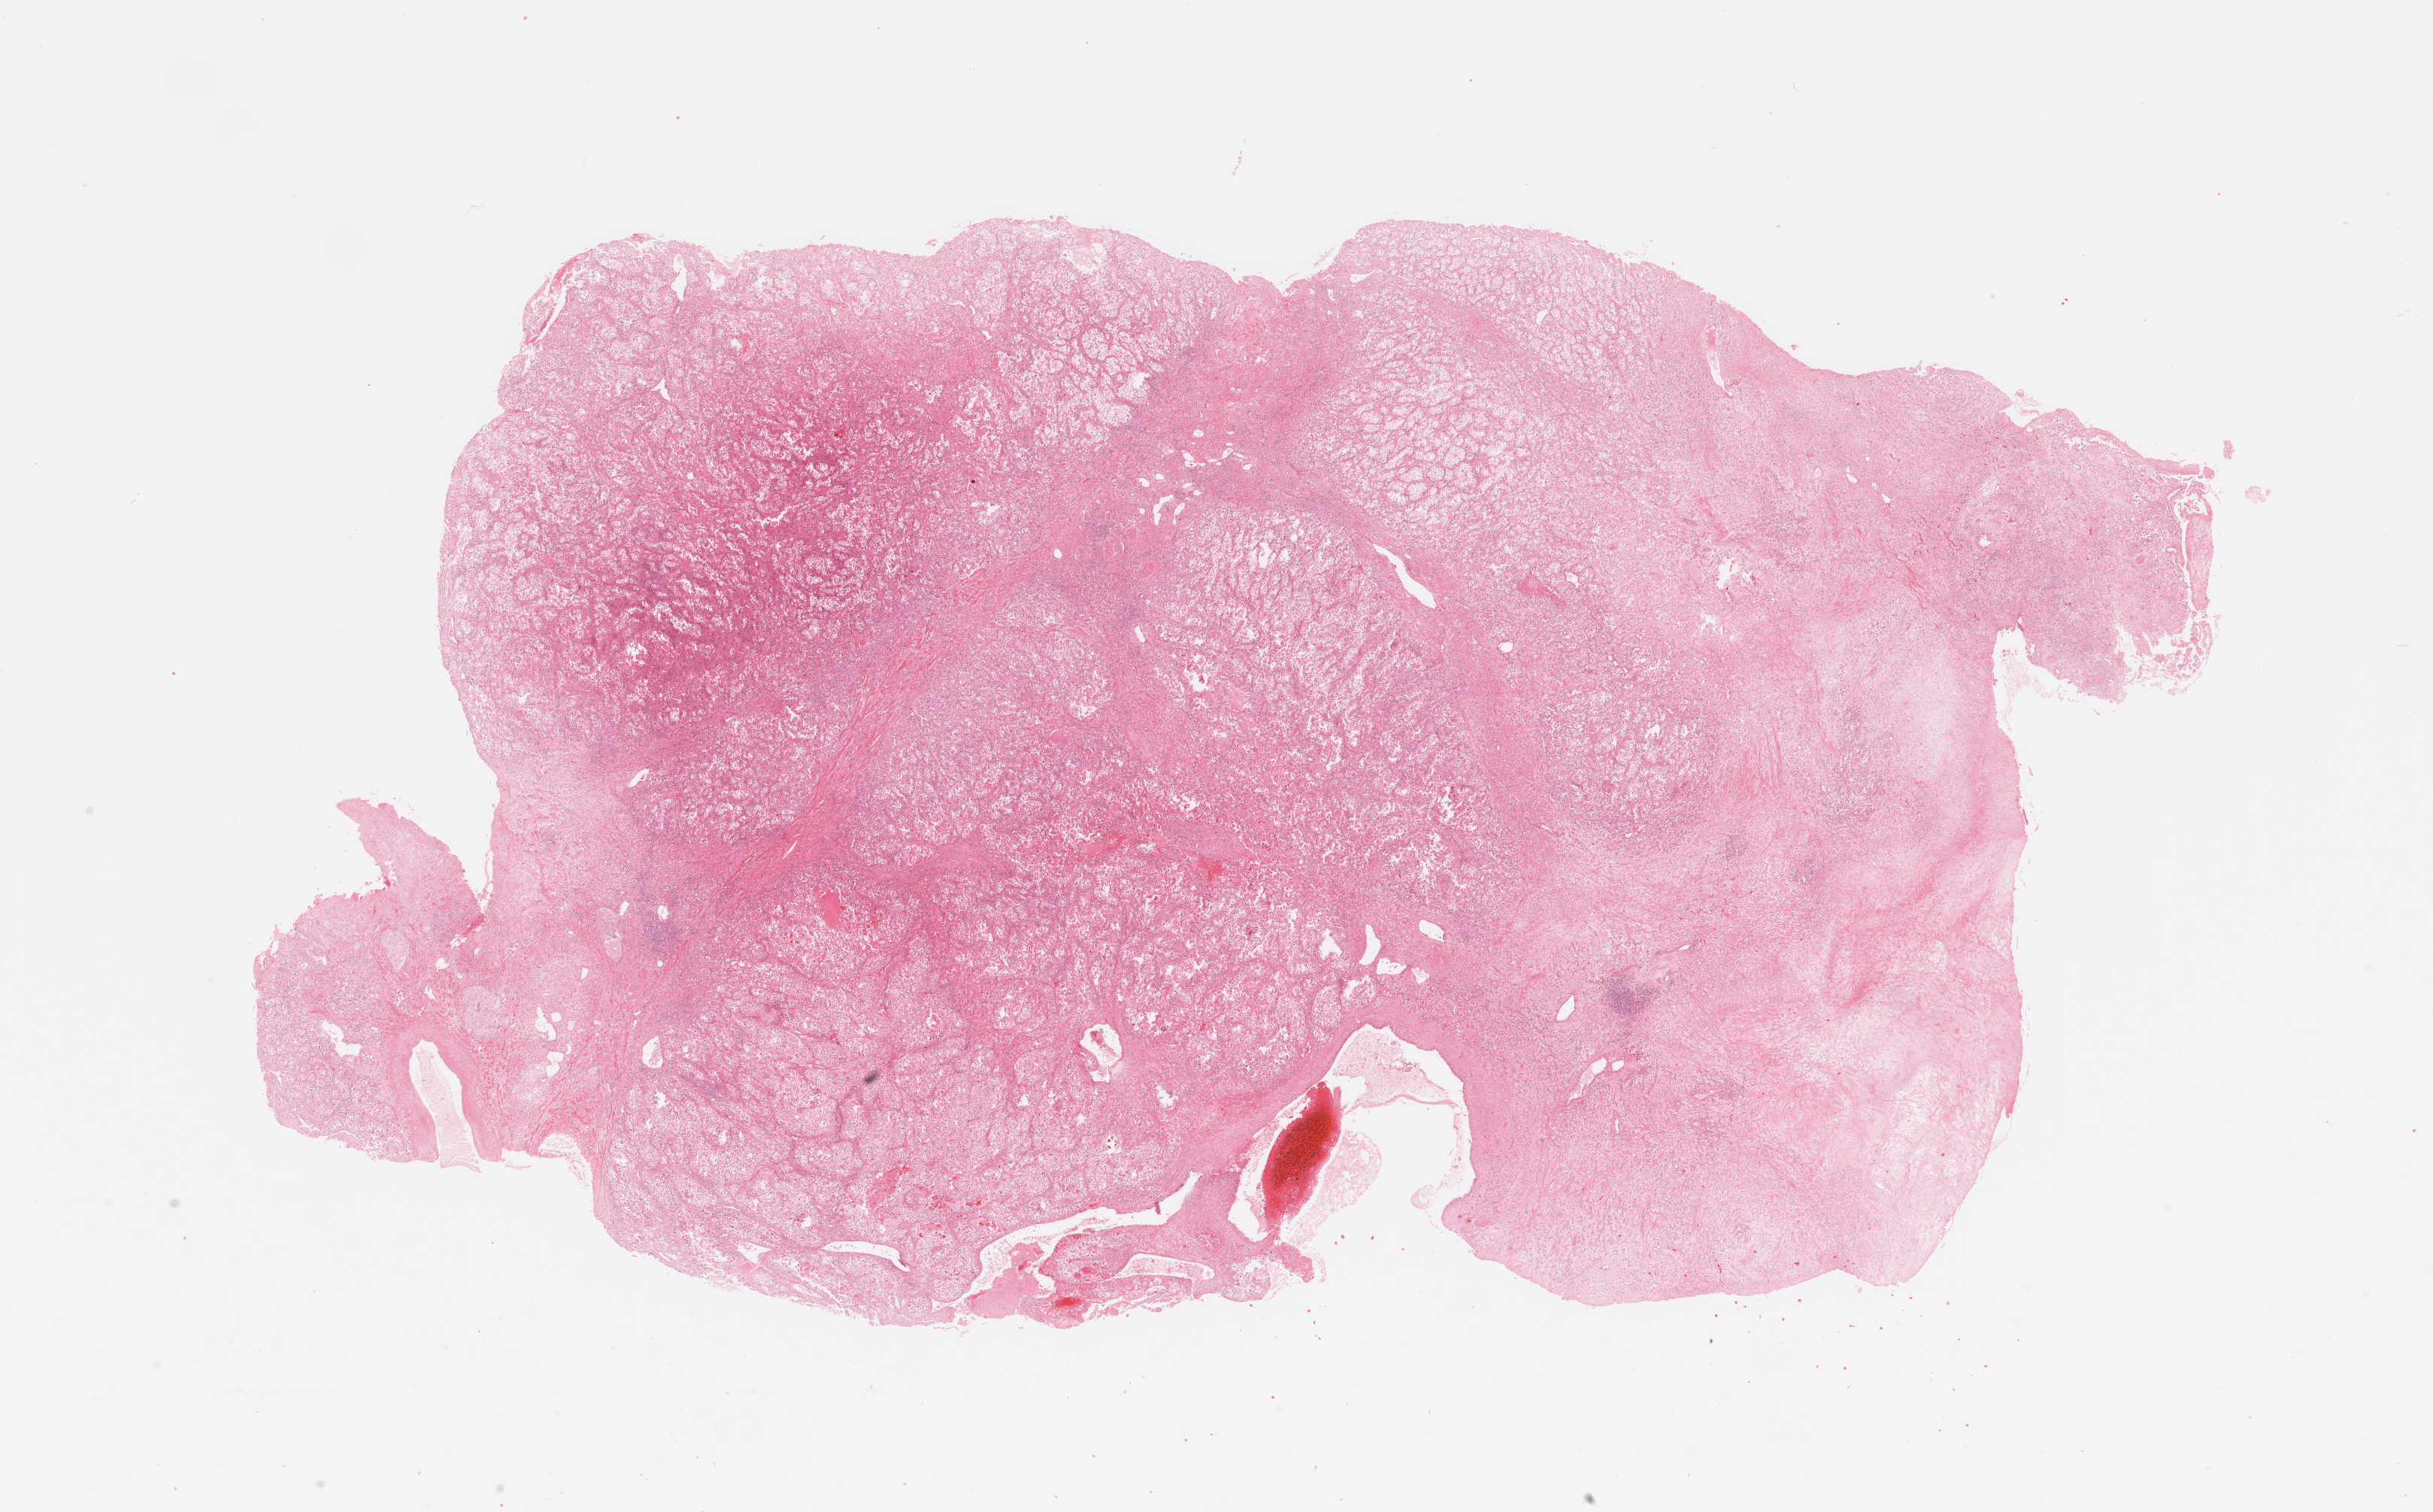
Digitized H&E tissue section (whole slide), a low-resolution overview of the entire scanned area, about 25.6 x 15.9 mm (from a 20x scan), kidney, tumour tissue. 60-year-old male patient.
Diagnosis: Renal cell carcinoma, NOS.